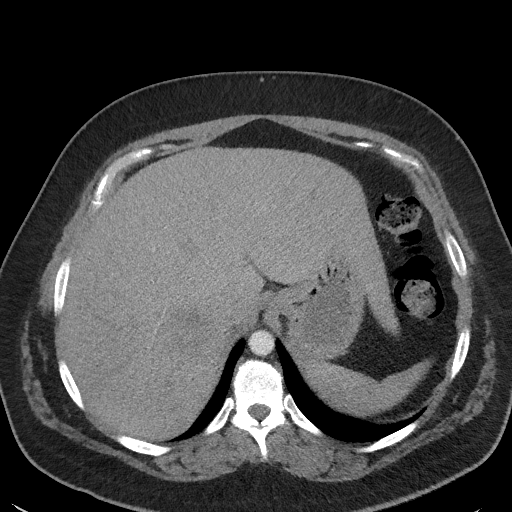
Contrast-enhanced abdominal CT, one axial slice. Slice 42 of 56 in the series (ordered by position). Reconstruction kernel I41f/3. Intravenous contrast given. Soft-tissue window (W 400 / L 40 HU). 5 mm slice thickness. 512 × 512 image matrix, field of view 373 × 373 mm. Female patient, age 35 years. From the clinical record (not read from this slice): diagnosis: adrenocortical carcinoma; tumour side: right adrenal; tumour size at pathology: 15 cm; Ki-67 index: 40 %; stage (as recorded): 2.
Structures marked on this image (semi-automatic segmentation, software-assisted and operator-edited):
- mass: box from (x=165, y=313) to (x=206, y=346) px